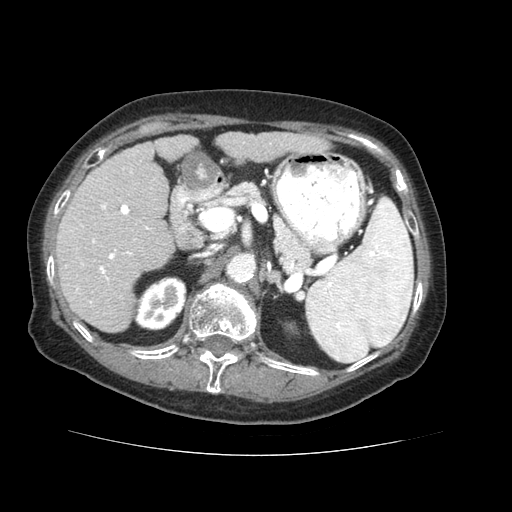
Contrast-enhanced abdominal CT (liver protocol), one axial slice. Slice 28 of 73 in the series (ordered by position). Soft-tissue window (W 400 / L 40 HU). 2.5 mm slice thickness. 512 × 512 image matrix, field of view 360 × 360 mm. From the clinical record (not read from this slice): diagnosis: hepatocellular carcinoma (patient treated with transarterial chemoembolisation; whether this scan precedes or follows treatment is not stated here); TNM stage (as recorded): Stage-IVB; Child-Pugh class: A; tumour nodularity: uninodular.
Annotated regions visible in this slice (semi-automatically segmented with operator editing):
- liver parenchyma outside the tumour (the mass and vessels are separate outlines, so this box may not span the whole liver): box from (x=54, y=132) to (x=326, y=332) px
- liver vessels: (x=65, y=168)–(x=150, y=303)